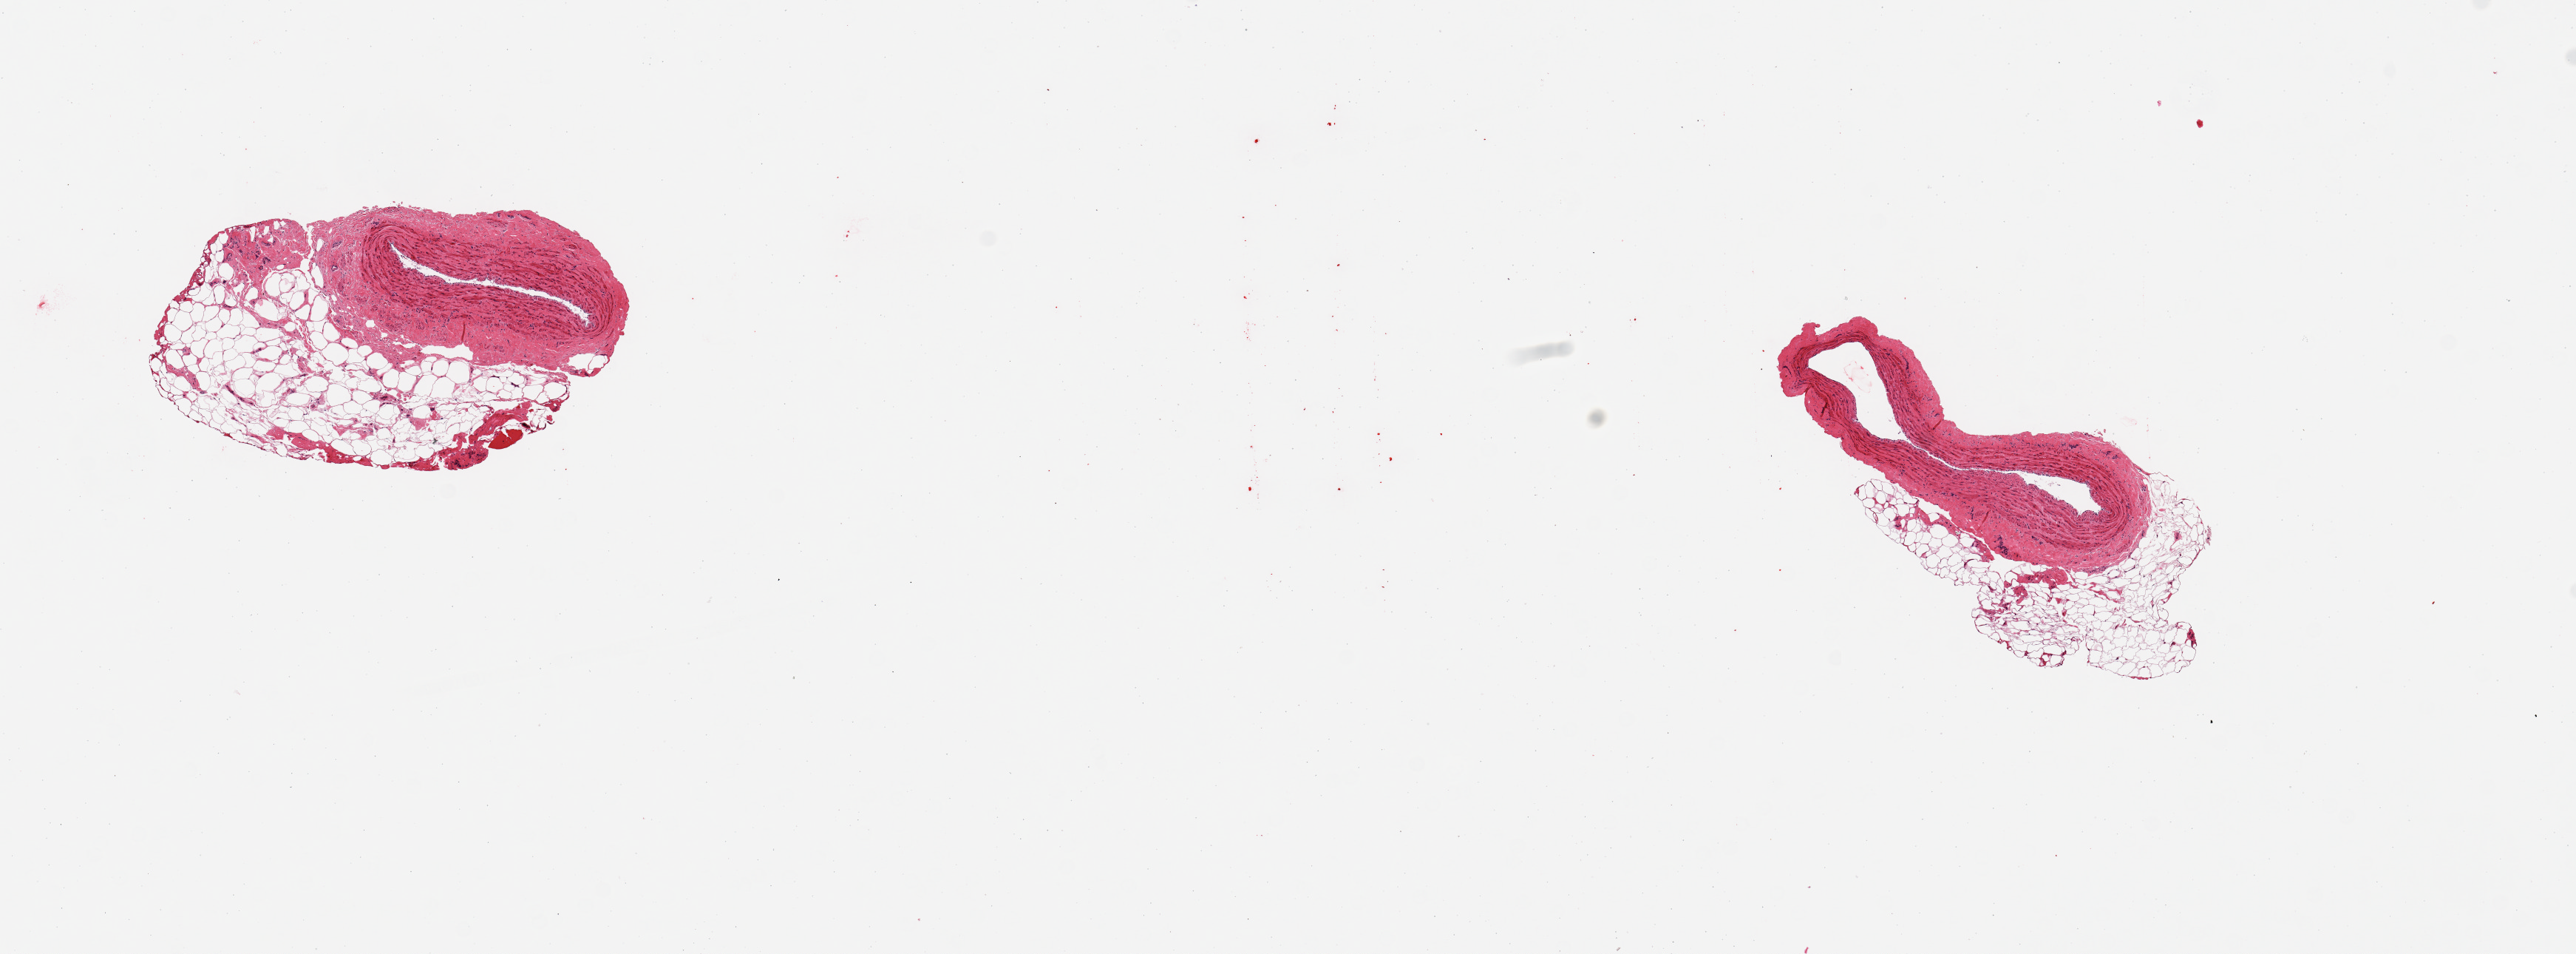
Whole-slide image, H&E stain — a low-resolution overview of the entire scanned area, about 13.8 x 5.1 mm, PAXgene-fixed paraffin-embedded (PFPE) section, target tissue: tibial artery, tissue donor sample. Male donor.
Review note (as recorded): 1 piece; well trimmed.